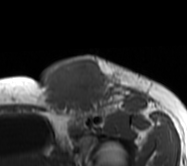
MRI of an extremity soft-tissue mass, one axial slice; position 42 of 62 along the scan axis; MR volume resampled by the dataset authors to the PET/CT grid (not the native acquisition matrix); 3.27 mm slice thickness; 187 × 166 image matrix, field of view 183 × 162 mm. Female patient. From the clinical record (not read from this slice): histological type: leiomyosarcoma; grade: high; site of the primary tumour: groin.
Annotated regions visible in this slice (expert contour drawn on MRI and transferred to this co-registered scan by the dataset authors):
- gross tumour volume including surrounding oedema: bounding box (x1, y1, x2, y2) in pixels: (39, 55, 152, 130)
- gross tumour volume (mass): (39, 56, 113, 118)